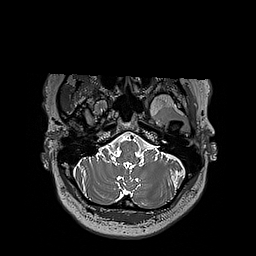
Brain MRI from a brain-tumour surgery series, one axial slice. Position 157 of 192 along the scan axis. 1 mm slice thickness. 256 × 256 image matrix, field of view 250 × 250 mm. From the clinical record (not read from this slice): histopathology: Oligodendroglioma; WHO grade: 3; IDH mutation: yes.
Annotated regions visible in this slice (expert manual segmentation):
- tumour: box from (x=124, y=93) to (x=197, y=113) px